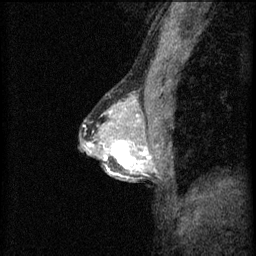
Breast MRI (dynamic contrast-enhanced), one sagittal slice. Slice 37 of 60 in the series (ordered by position). 3 images stored at this slice position (order not interpretable as contrast timing). 1.5 T. TE 4.2 ms, TR 8.2 ms. 2 mm slice thickness. 256 × 256 image matrix, field of view 180 × 180 mm. Female patient, age 44 years.
Annotated regions visible in this slice (semi-automatic segmentation, software-assisted and operator-edited):
- analysis volume of interest (the breast-tissue region the enhancement analysis was run in; not a lesion): bounding box [x1, y1, x2, y2] px = [102, 132, 151, 181]
- tumour enhancement mask (voxels above the 70 % enhancement threshold inside the analysis volume of interest): [104, 140, 151, 179]